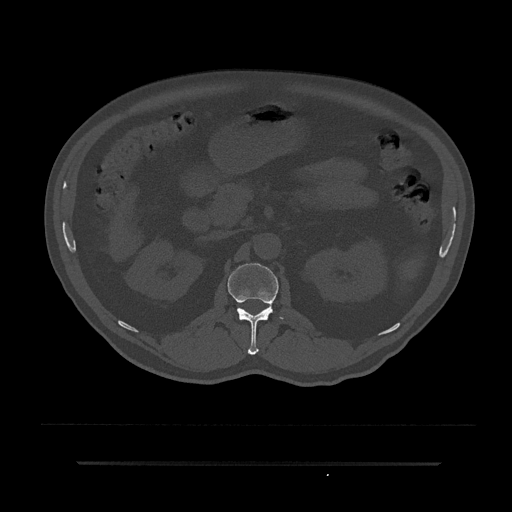
CT including the spine, one axial slice; slice 138 of 797 in the series (ordered by position); reconstruction kernel Br40s/3; bone window (W 1800 / L 400 HU); 0.5 mm slice thickness; 512 × 512 image matrix, field of view 464 × 464 mm. Male patient, age 59 years. From the clinical record (not read from this slice): primary cancer: bile ducts; vertebrae with lytic lesions (as recorded): T10.
Annotated regions visible in this slice (semi-automatic segmentation, software-assisted and operator-edited):
- L1 vertebra: bounding box <228,263,283,355> (left, top, right, bottom; pixels)